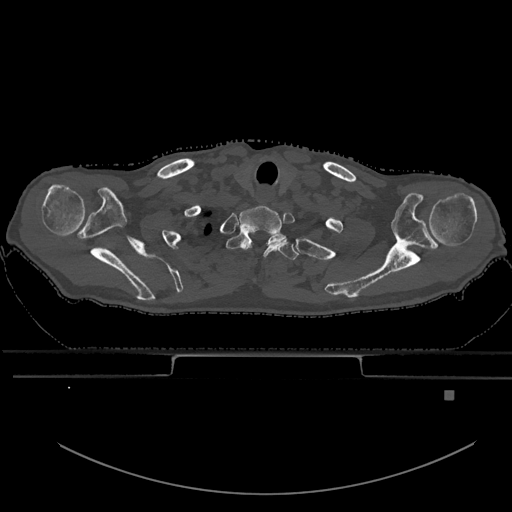
CT including the spine, one axial slice; slice 551 of 969 in the series (ordered by position); bone window (W 1800 / L 400 HU); 0.5 mm slice thickness; 512 × 512 image matrix, field of view 456 × 456 mm. Male patient, age 82 years. Case-level facts recorded for this patient, not image findings: primary cancer: prostate; vertebrae with lytic lesions (as recorded): T11, T9, T8, T2.
Annotated regions visible in this slice (semi-automatically segmented with operator editing):
- T1 vertebra: bounding box [x1, y1, x2, y2] px = [226, 231, 299, 260]